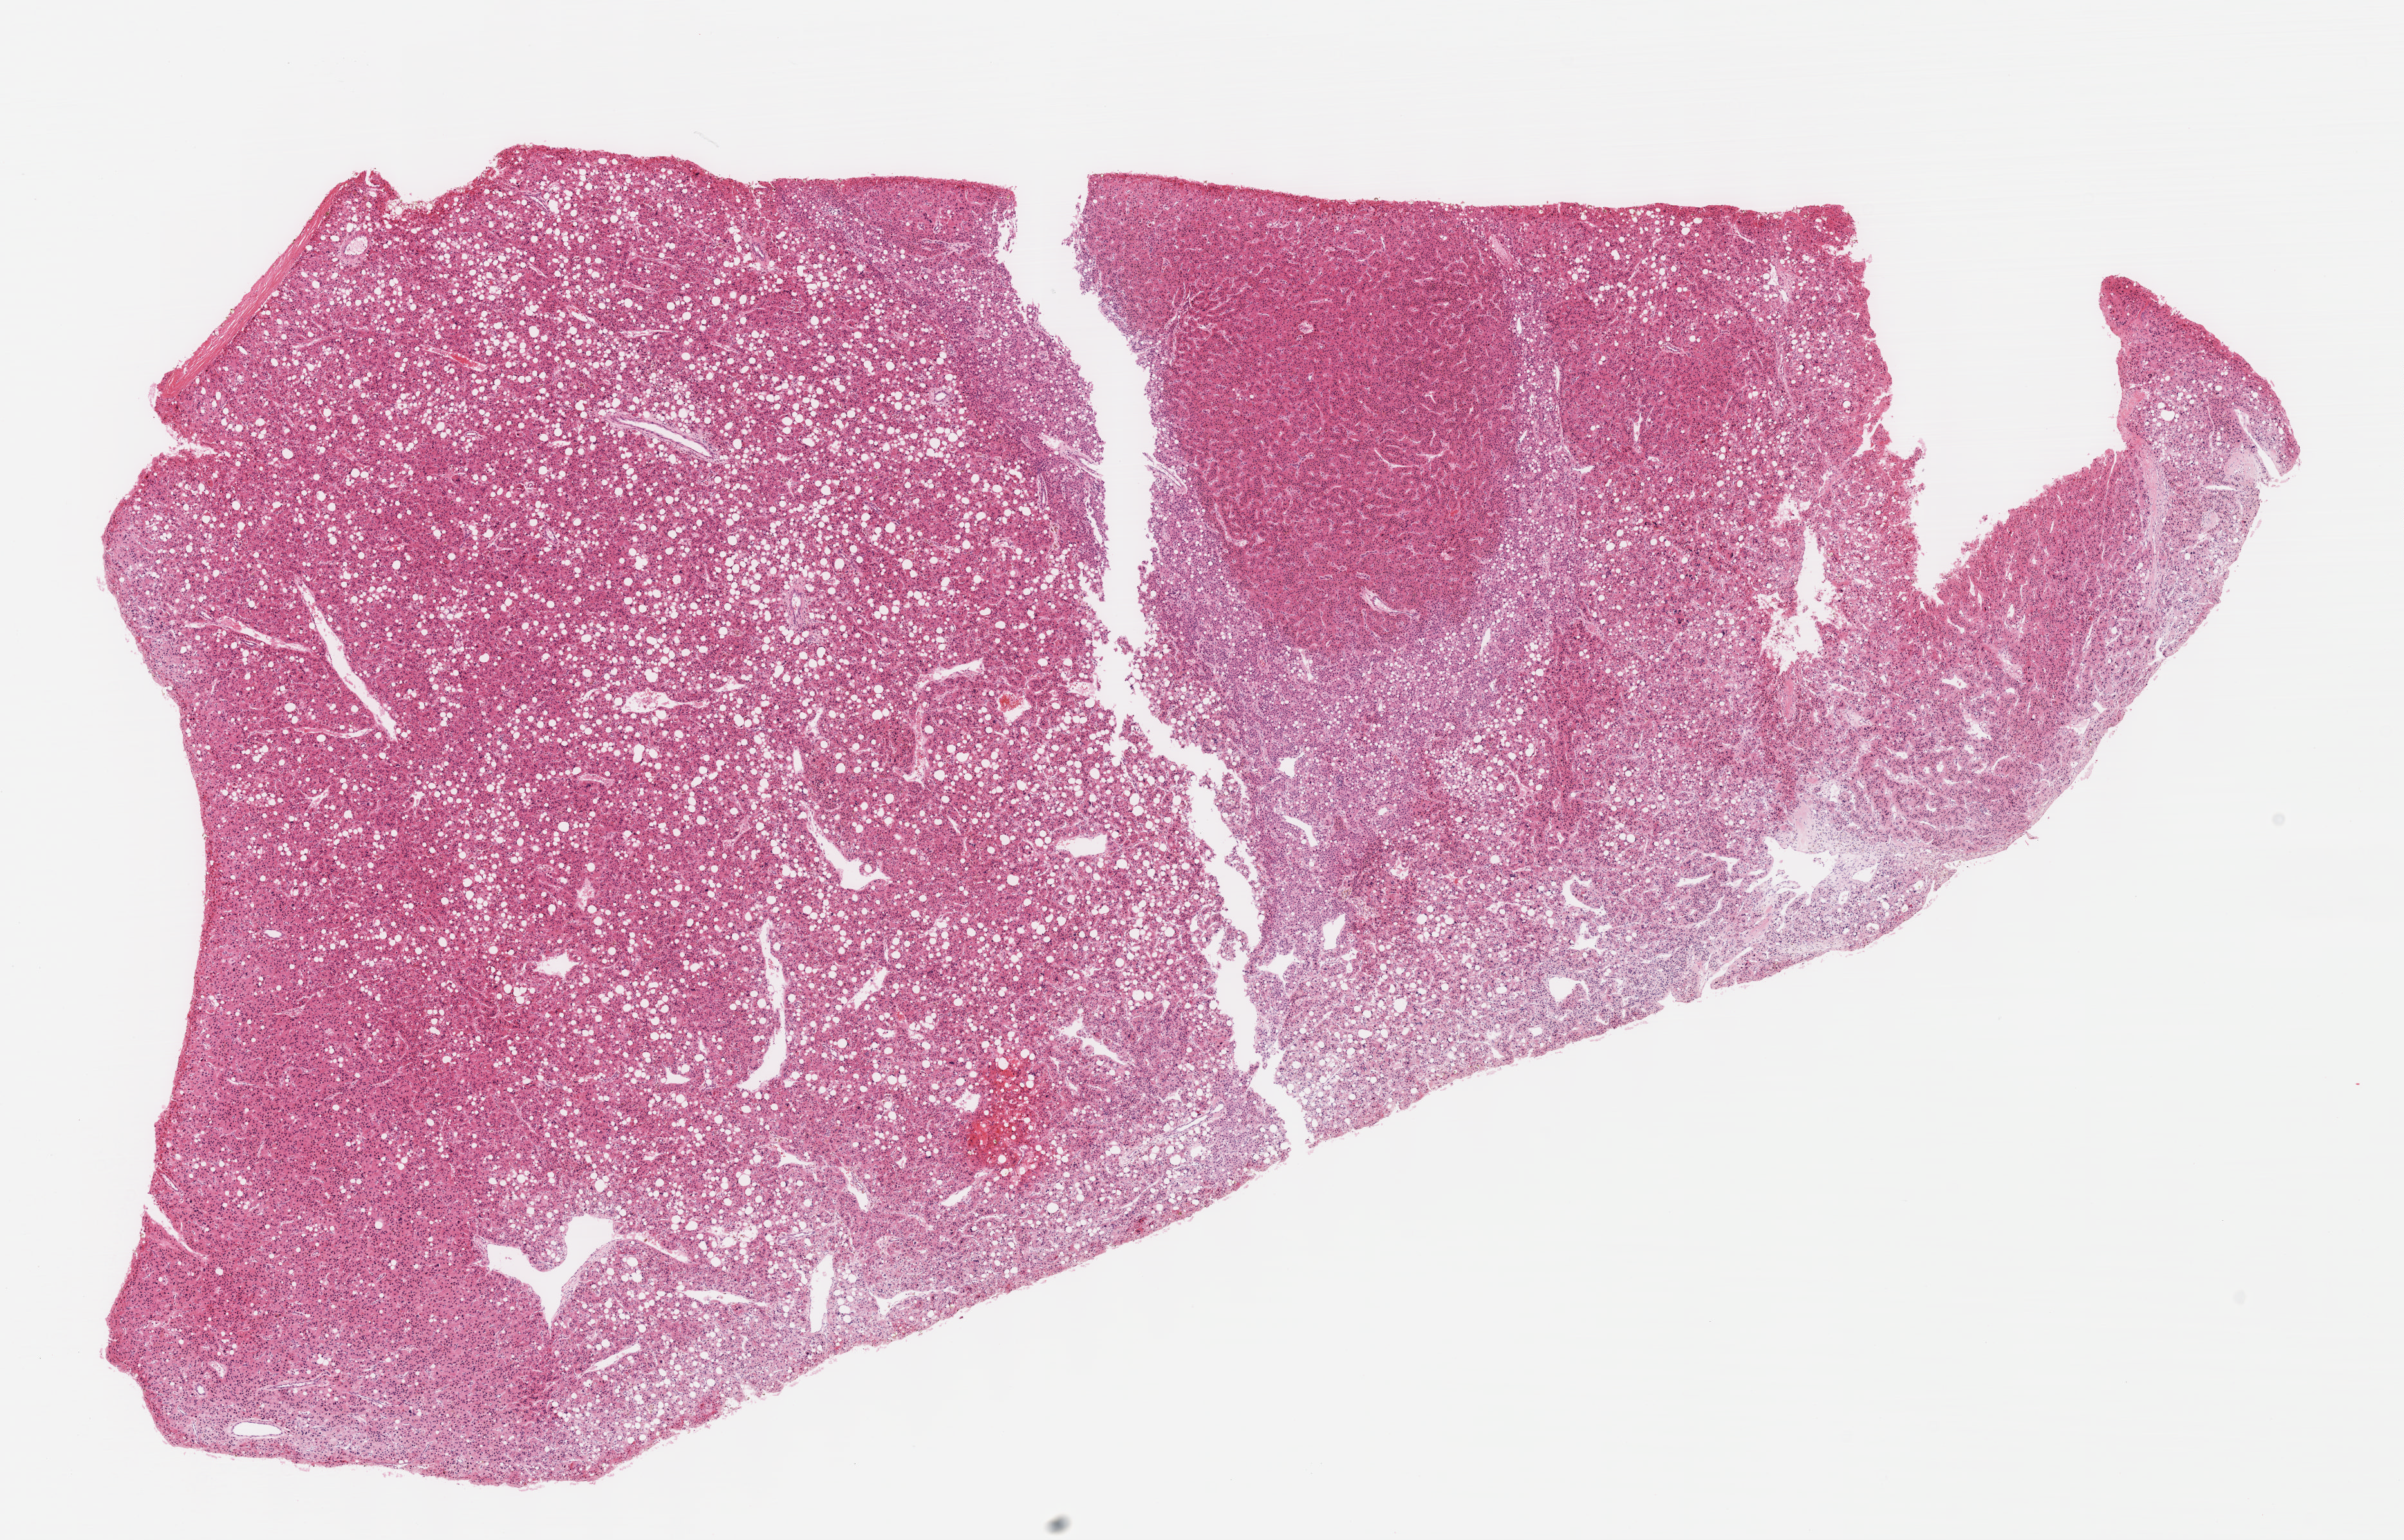
Digitized Hematoxylin and eosin (H&E) stained tissue section (whole slide), low-resolution overview of the scanned area, about 15.1 x 9.7 mm; formalin-fixed paraffin-embedded (FFPE) diagnostic section; liver, primary tumour sample. Male, age 60 years at initial diagnosis.
Diagnosis: Hepatocellular carcinoma, NOS.